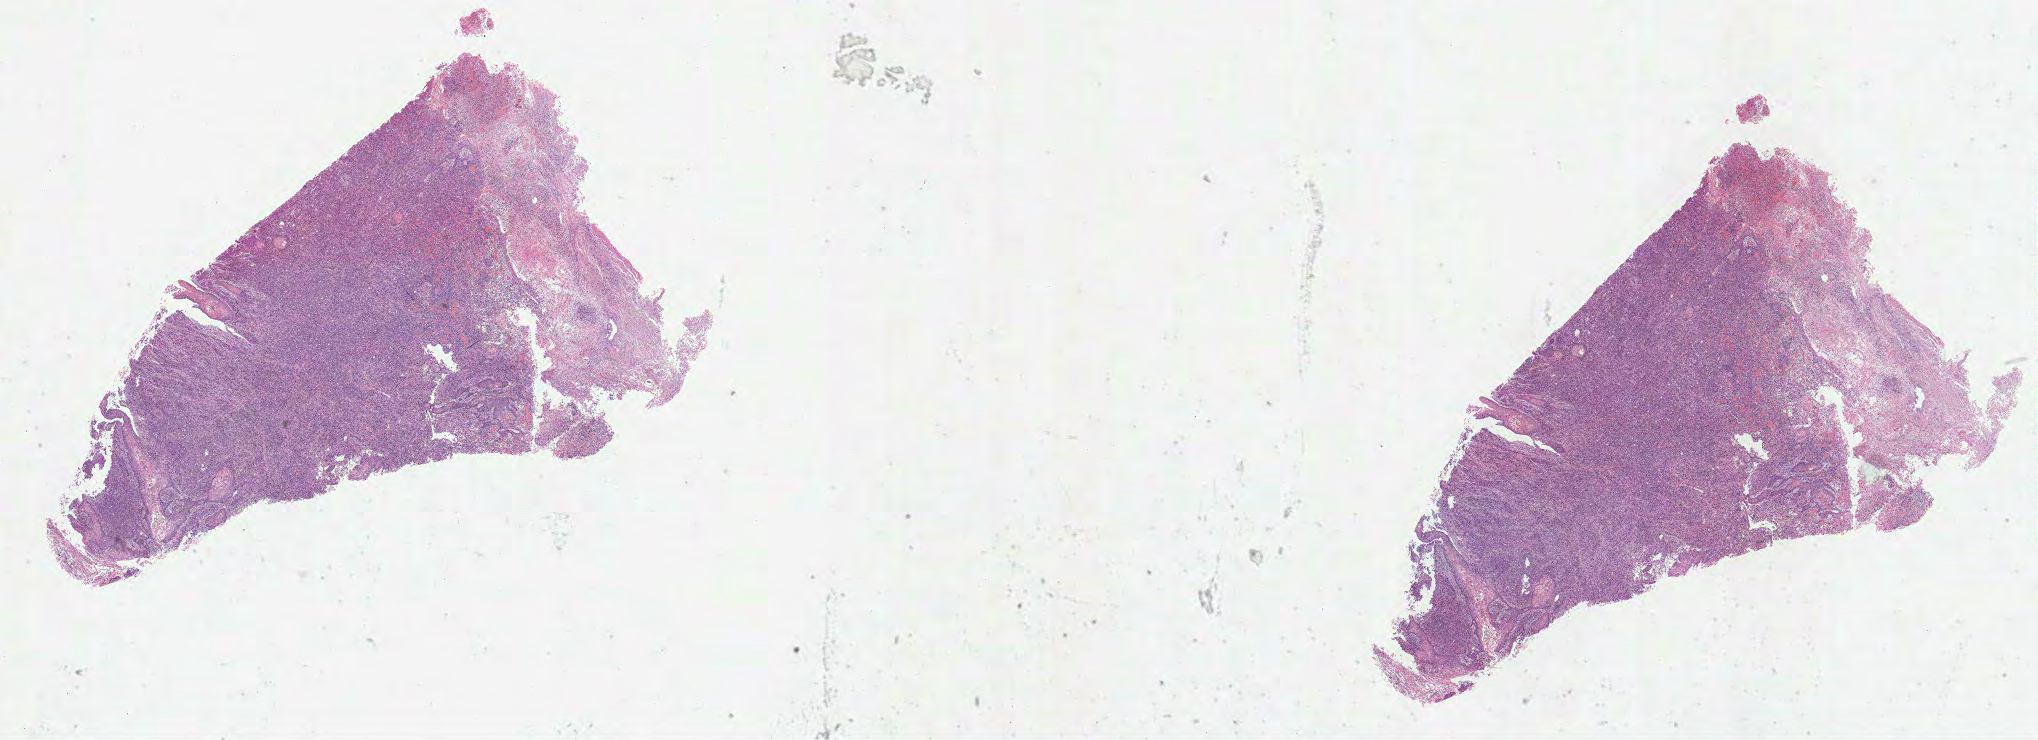
Whole-slide histology image, H&E-stained — low-resolution overview of the scanned area, about 32.9 x 11.9 mm, formalin-fixed paraffin-embedded (FFPE) diagnostic section, lung, primary tumour sample. Male, age 85 years at initial diagnosis.
Pathologic diagnosis: Squamous cell carcinoma, NOS. AJCC pathologic stage: IB. TNM: T2 N0 MX.